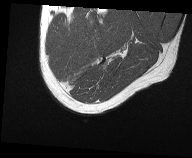
MRI of an extremity soft-tissue mass, one axial slice. Slice 4 of 61 in the series (ordered by position). MR volume resampled by the dataset authors to the PET/CT grid (not the native acquisition matrix). 3.27 mm slice thickness. 192 × 158 image matrix, field of view 187 × 154 mm. Male patient. From the clinical record (not read from this slice): histological type: pleiomorphic liposarcoma; grade: high; site of the primary tumour: left thigh.
Annotated regions visible in this slice (expert contour drawn on MRI and transferred to this co-registered scan by the dataset authors):
- gross tumour volume including surrounding oedema: bounding box <86,25,104,35> (left, top, right, bottom; pixels)